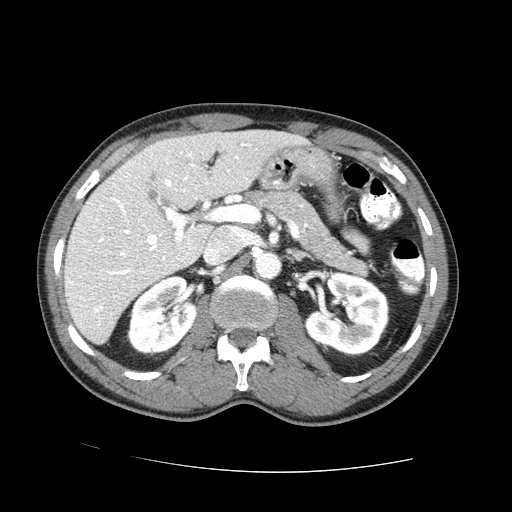
Contrast-enhanced abdominal CT (liver protocol), one axial slice. Slice 38 of 73 in the series (ordered by position). One of 2 acquisitions stored at this slice position. Soft-tissue window (W 400 / L 40 HU). 512 × 512 image matrix, field of view 380 × 380 mm. From the clinical record (not read from this slice): diagnosis: hepatocellular carcinoma (patient treated with transarterial chemoembolisation; whether this scan precedes or follows treatment is not stated here); TNM stage (as recorded): Stage-IVA; Child-Pugh class: A; tumour nodularity: uninodular.
Structures marked on this image (semi-automatic segmentation, software-assisted and operator-edited):
- liver parenchyma outside the tumour (the mass and vessels are separate outlines, so this box may not span the whole liver): bounding box [x1, y1, x2, y2] px = [64, 130, 309, 344]
- mass: [148, 170, 157, 199]
- liver vessels: [70, 144, 245, 312]